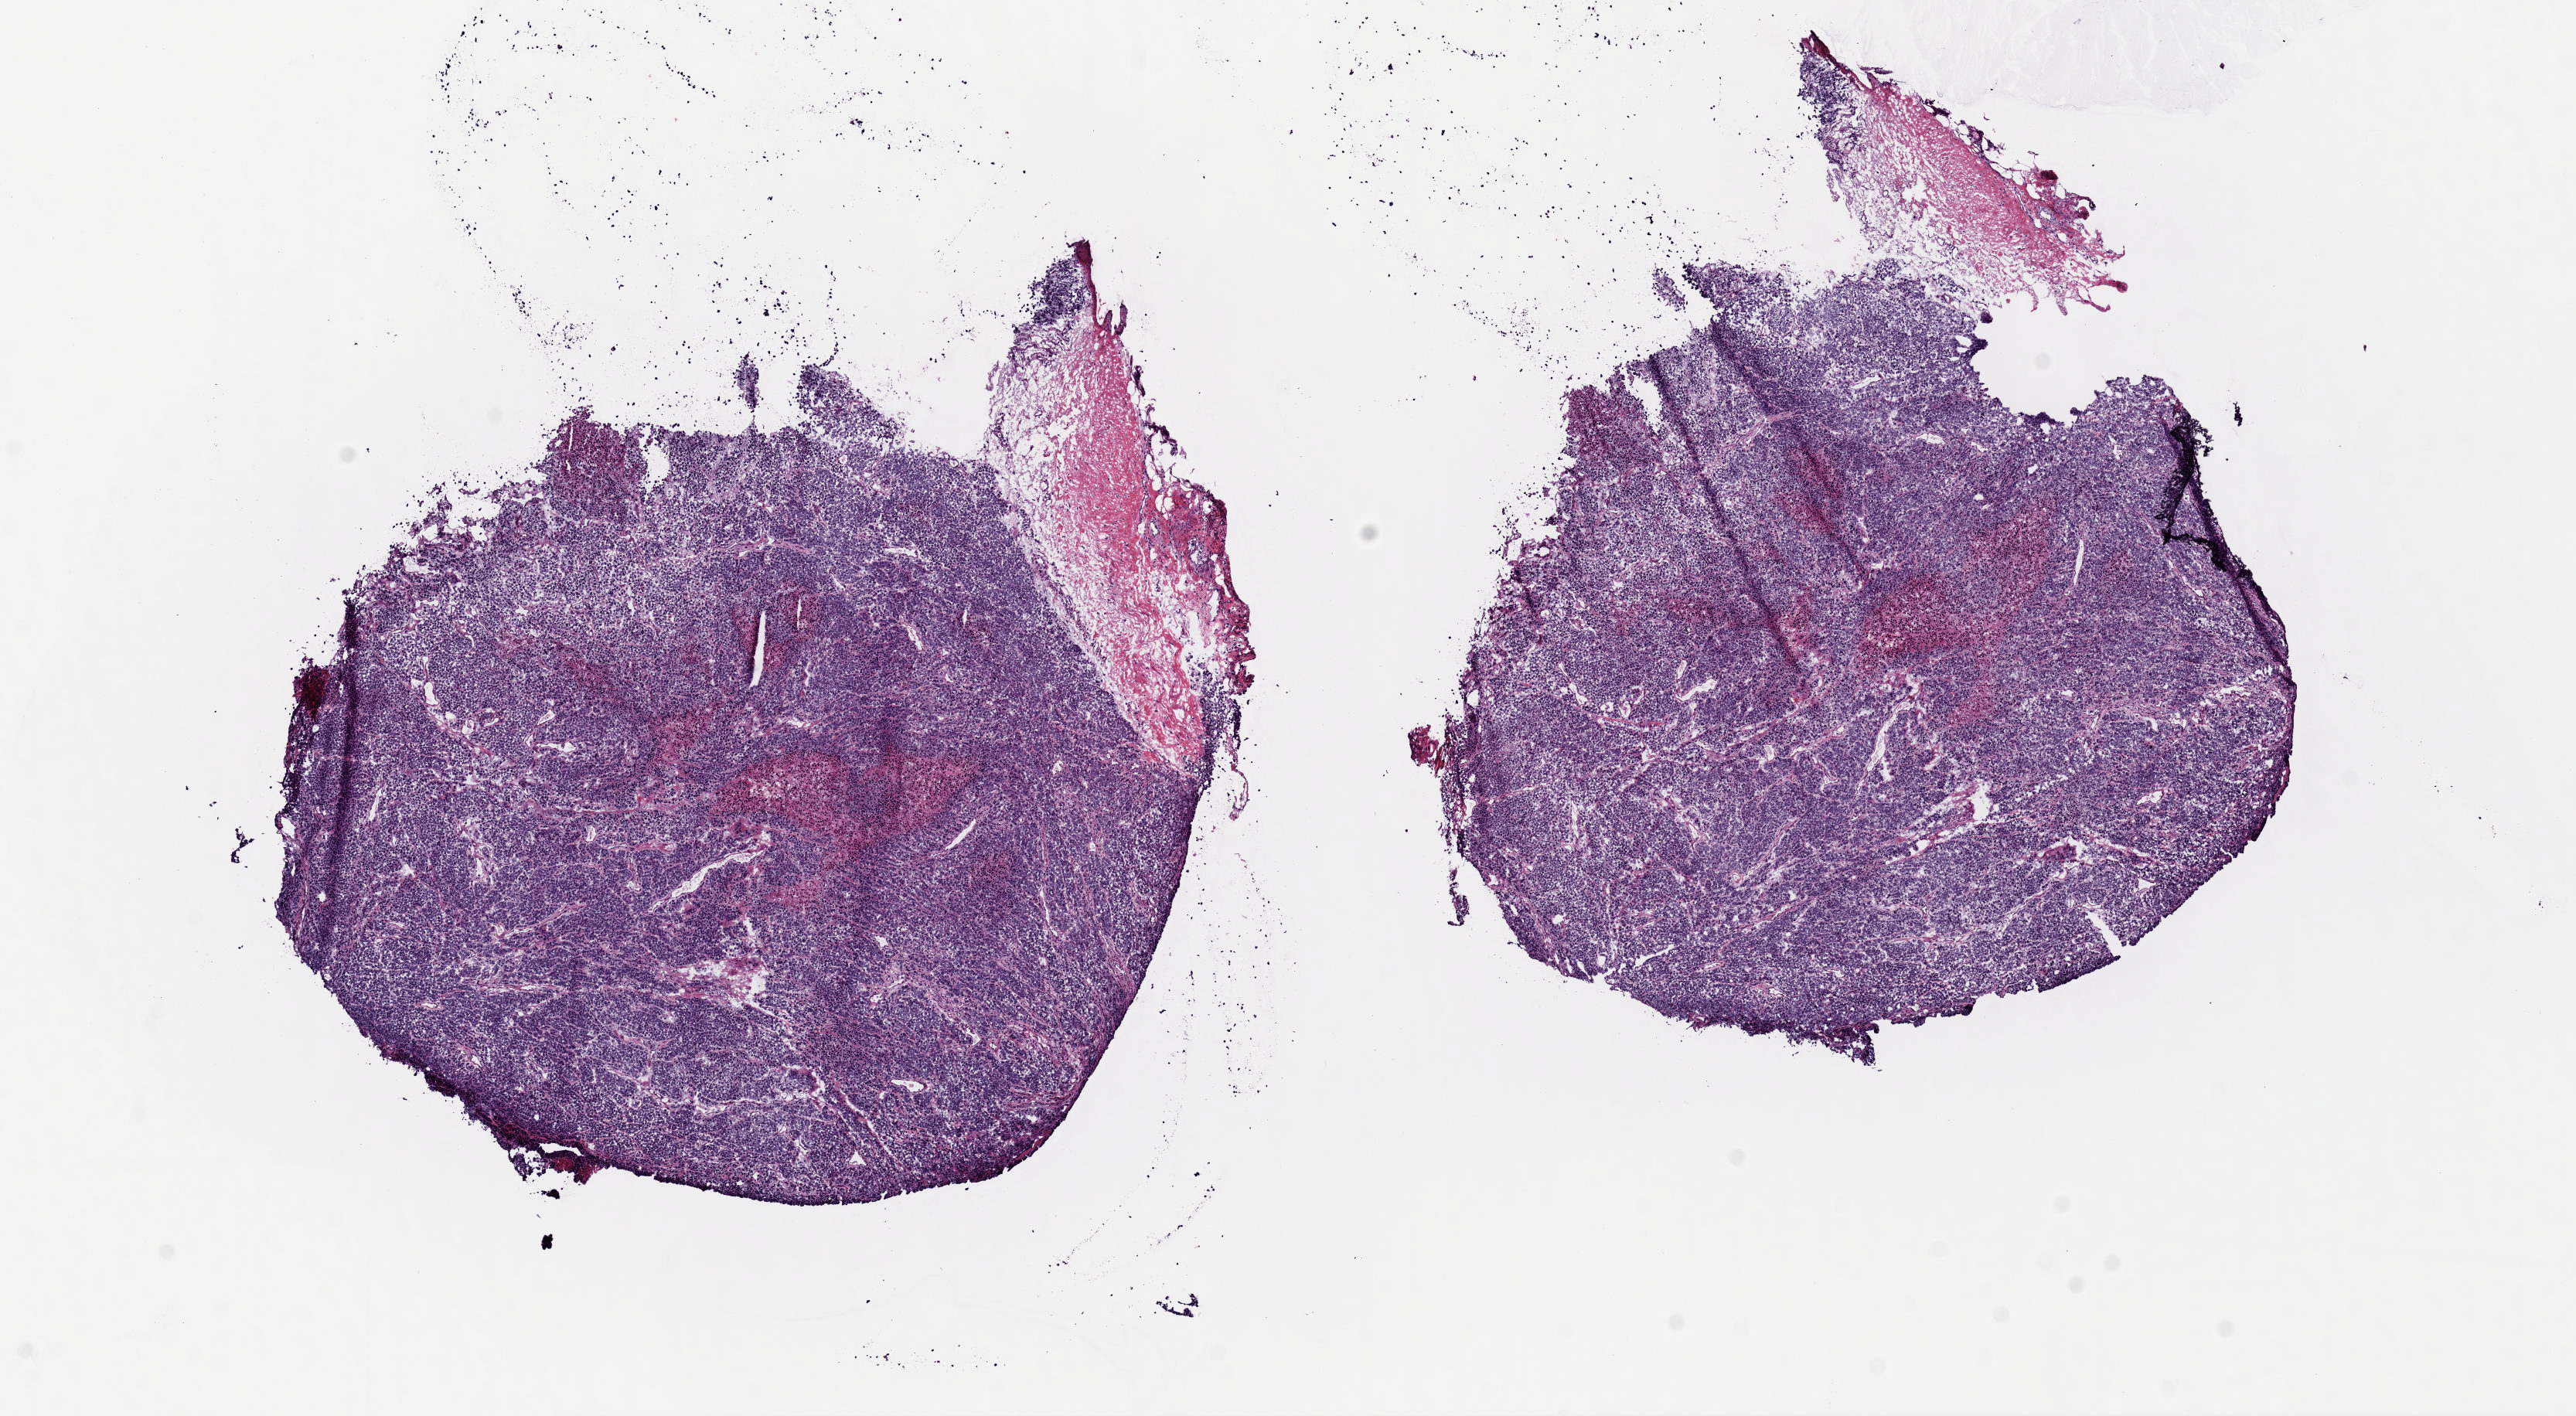
Digitized H&E tissue section (whole slide) — a low-resolution overview of the entire scanned area, about 13.2 x 7.2 mm. Frozen section from the top of the tissue portion. Metastatic tumour sample, sampled site: skin. Female patient; age at initial diagnosis 70 years. Pathologist review of this section (percent, as recorded): tumour cells 85%, tumour nuclei 90%, normal cells 0%, stromal cells 10%, necrosis 5%. Infiltration values recorded for this section: lymphocyte infiltration 0%, monocyte infiltration 0%, neutrophil infiltration 0%.
This section: metastatic tumour tissue. Patient diagnosis: Malignant melanoma, NOS.